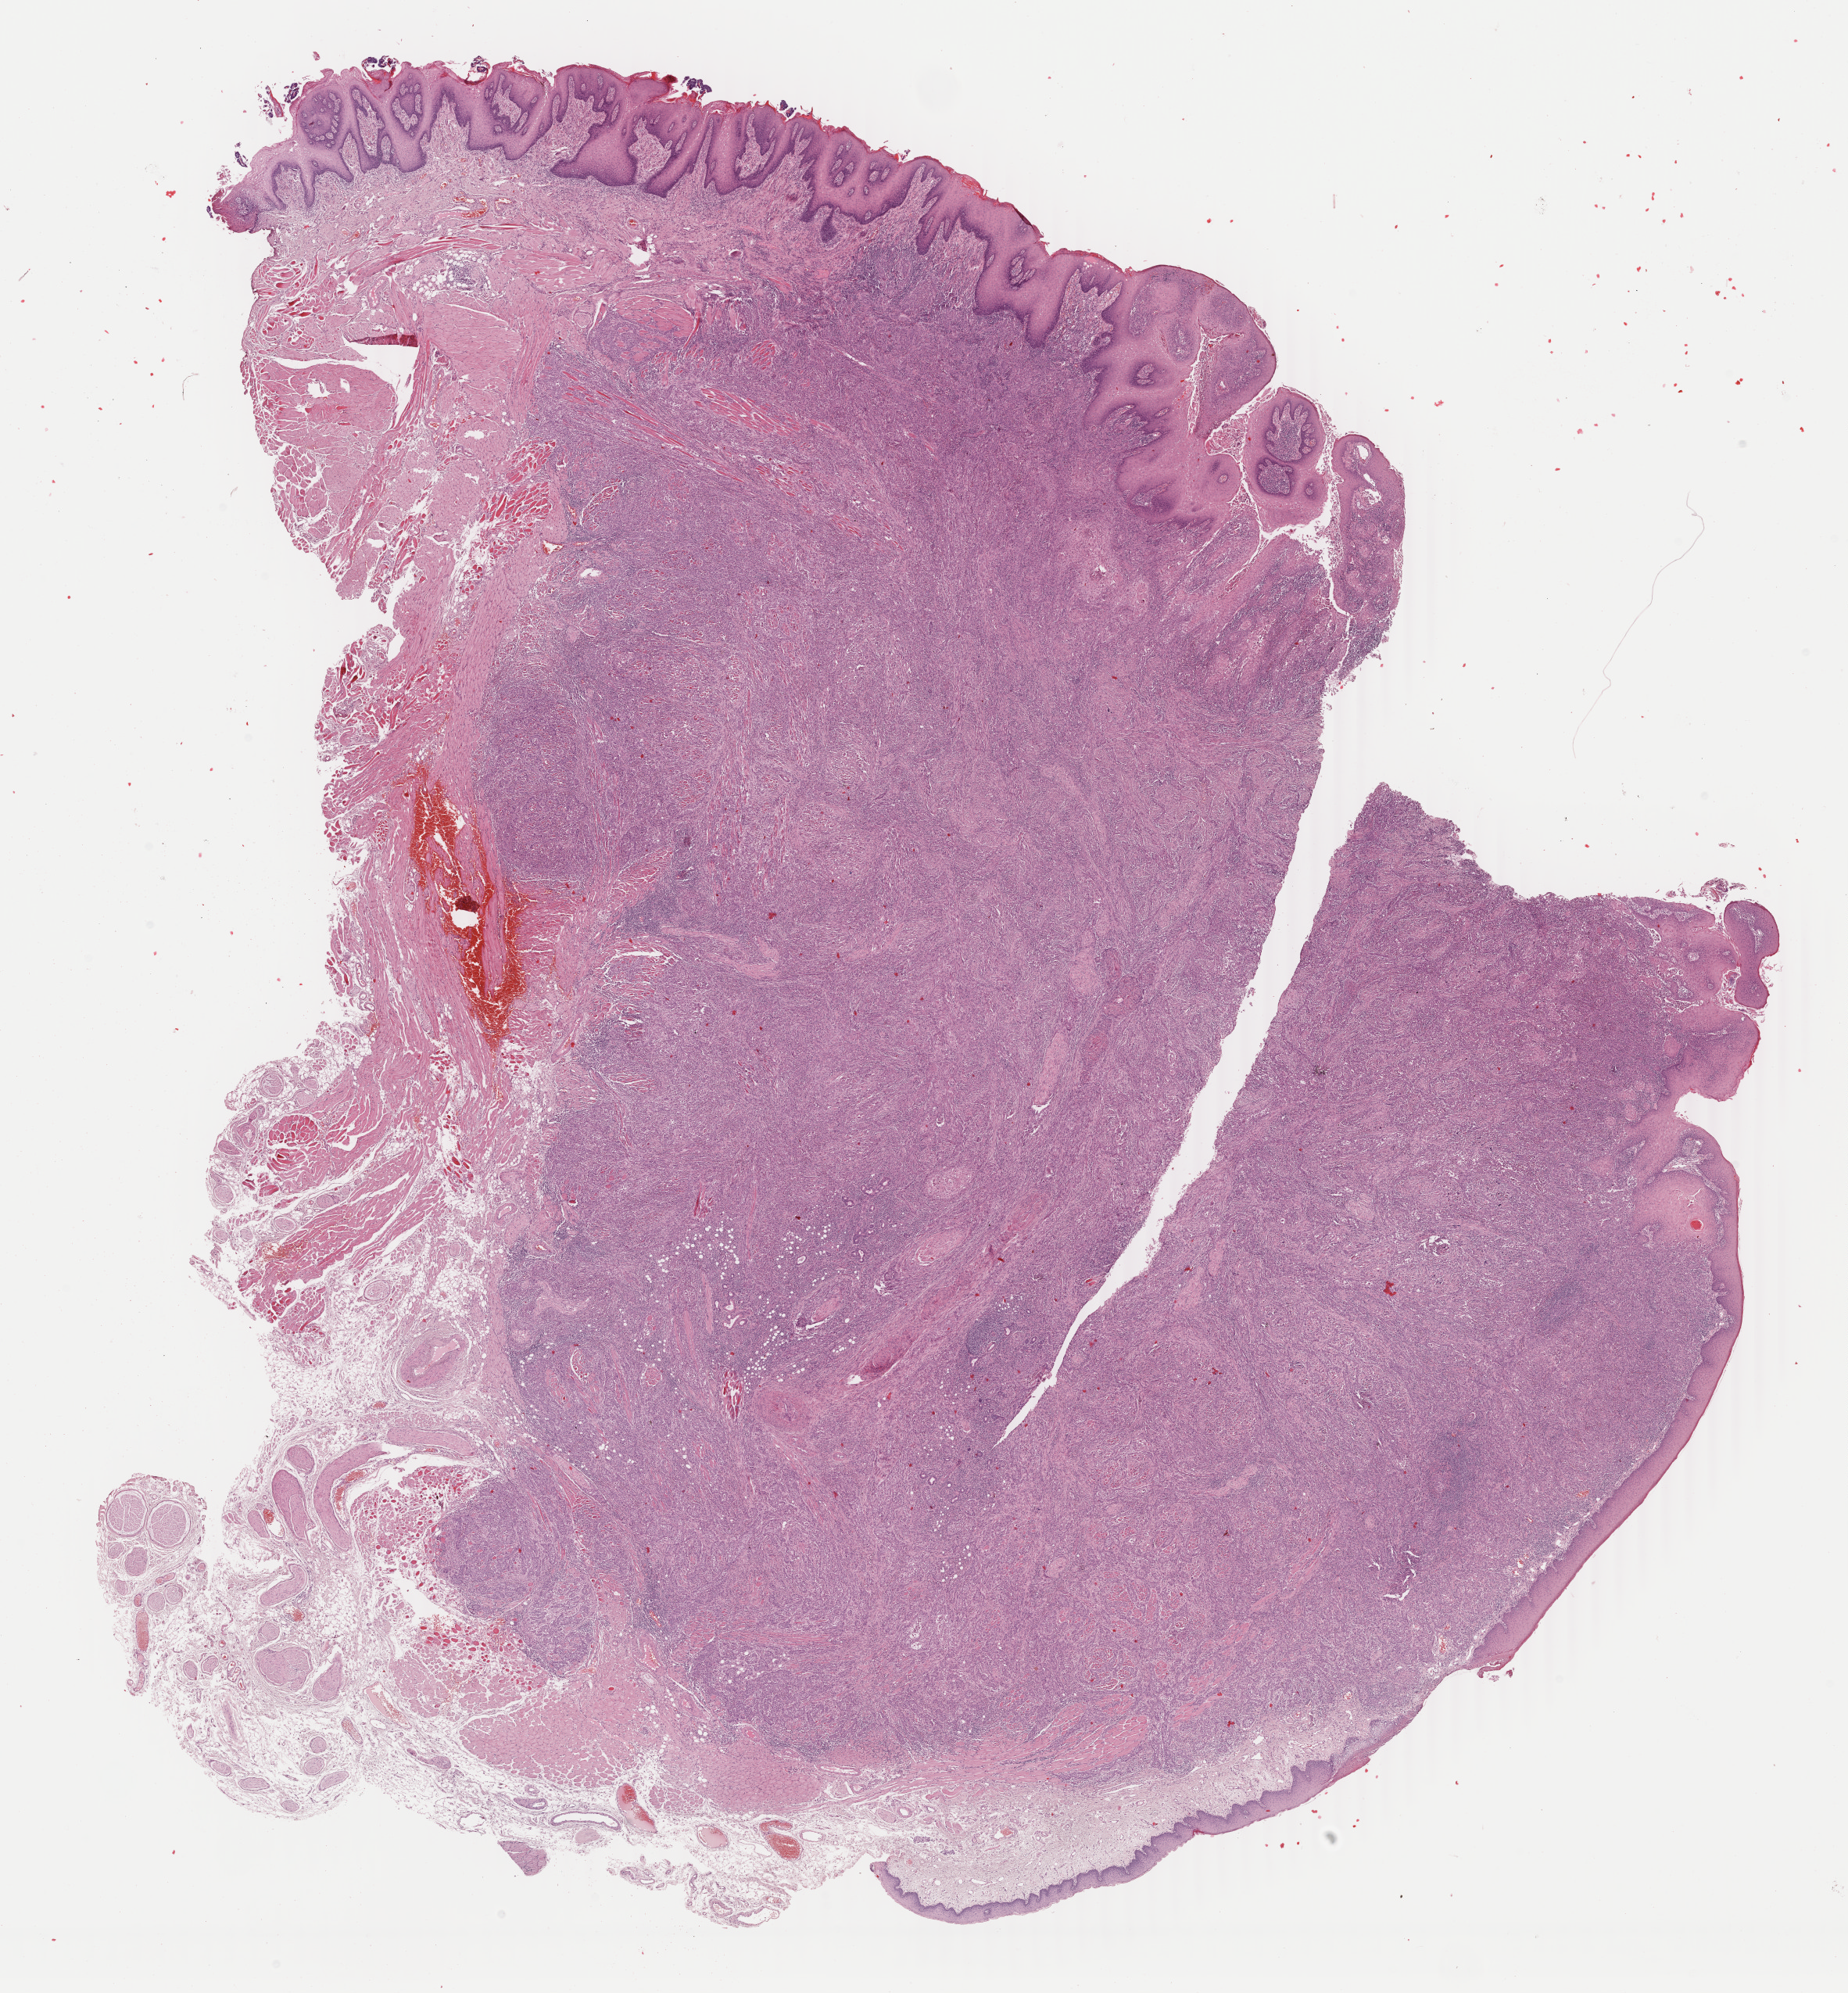
Digitized Hematoxylin and eosin (H&E) stained tissue section (whole slide), whole scanned area (about 18.8 x 20.3 mm, slide scanned at 40x) shown as a low-resolution overview. Formalin-fixed paraffin-embedded (FFPE) diagnostic section. Primary tumour sample from the head and neck. Female patient; age at initial diagnosis 82 years. Histologic grade: G3 (poorly differentiated).
* AJCC pathologic stage: II (7th edition)
* laterality: midline
* TNM: T2 N0
* histologic diagnosis: Squamous cell carcinoma, NOS (tongue, NOS)